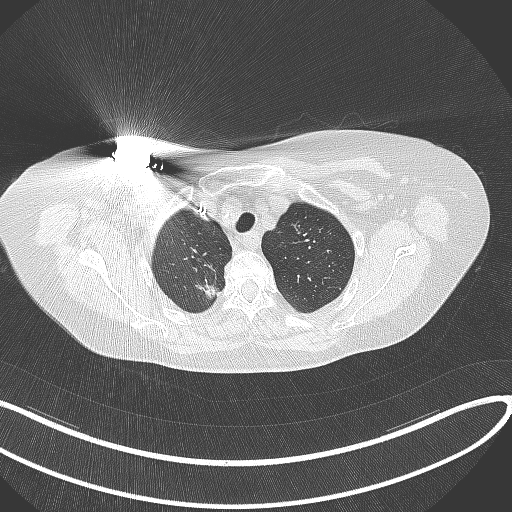
Chest CT, one axial slice. Position 282 of 316 along the scan axis. 120 kVp. Lung window (W 1500 / L -600 HU). 512 × 512 image matrix, field of view 400 × 400 mm. Female patient, age 72 years. Case-level facts recorded for this patient, not image findings: clinical TNM (as recorded): T1c N0 M0.
Outlined on this slice (rectangle marked by the reading radiologist):
- lung tumour (recorded histology: adenocarcinoma): bounding box (x1, y1, x2, y2) in pixels: (190, 278, 222, 301)